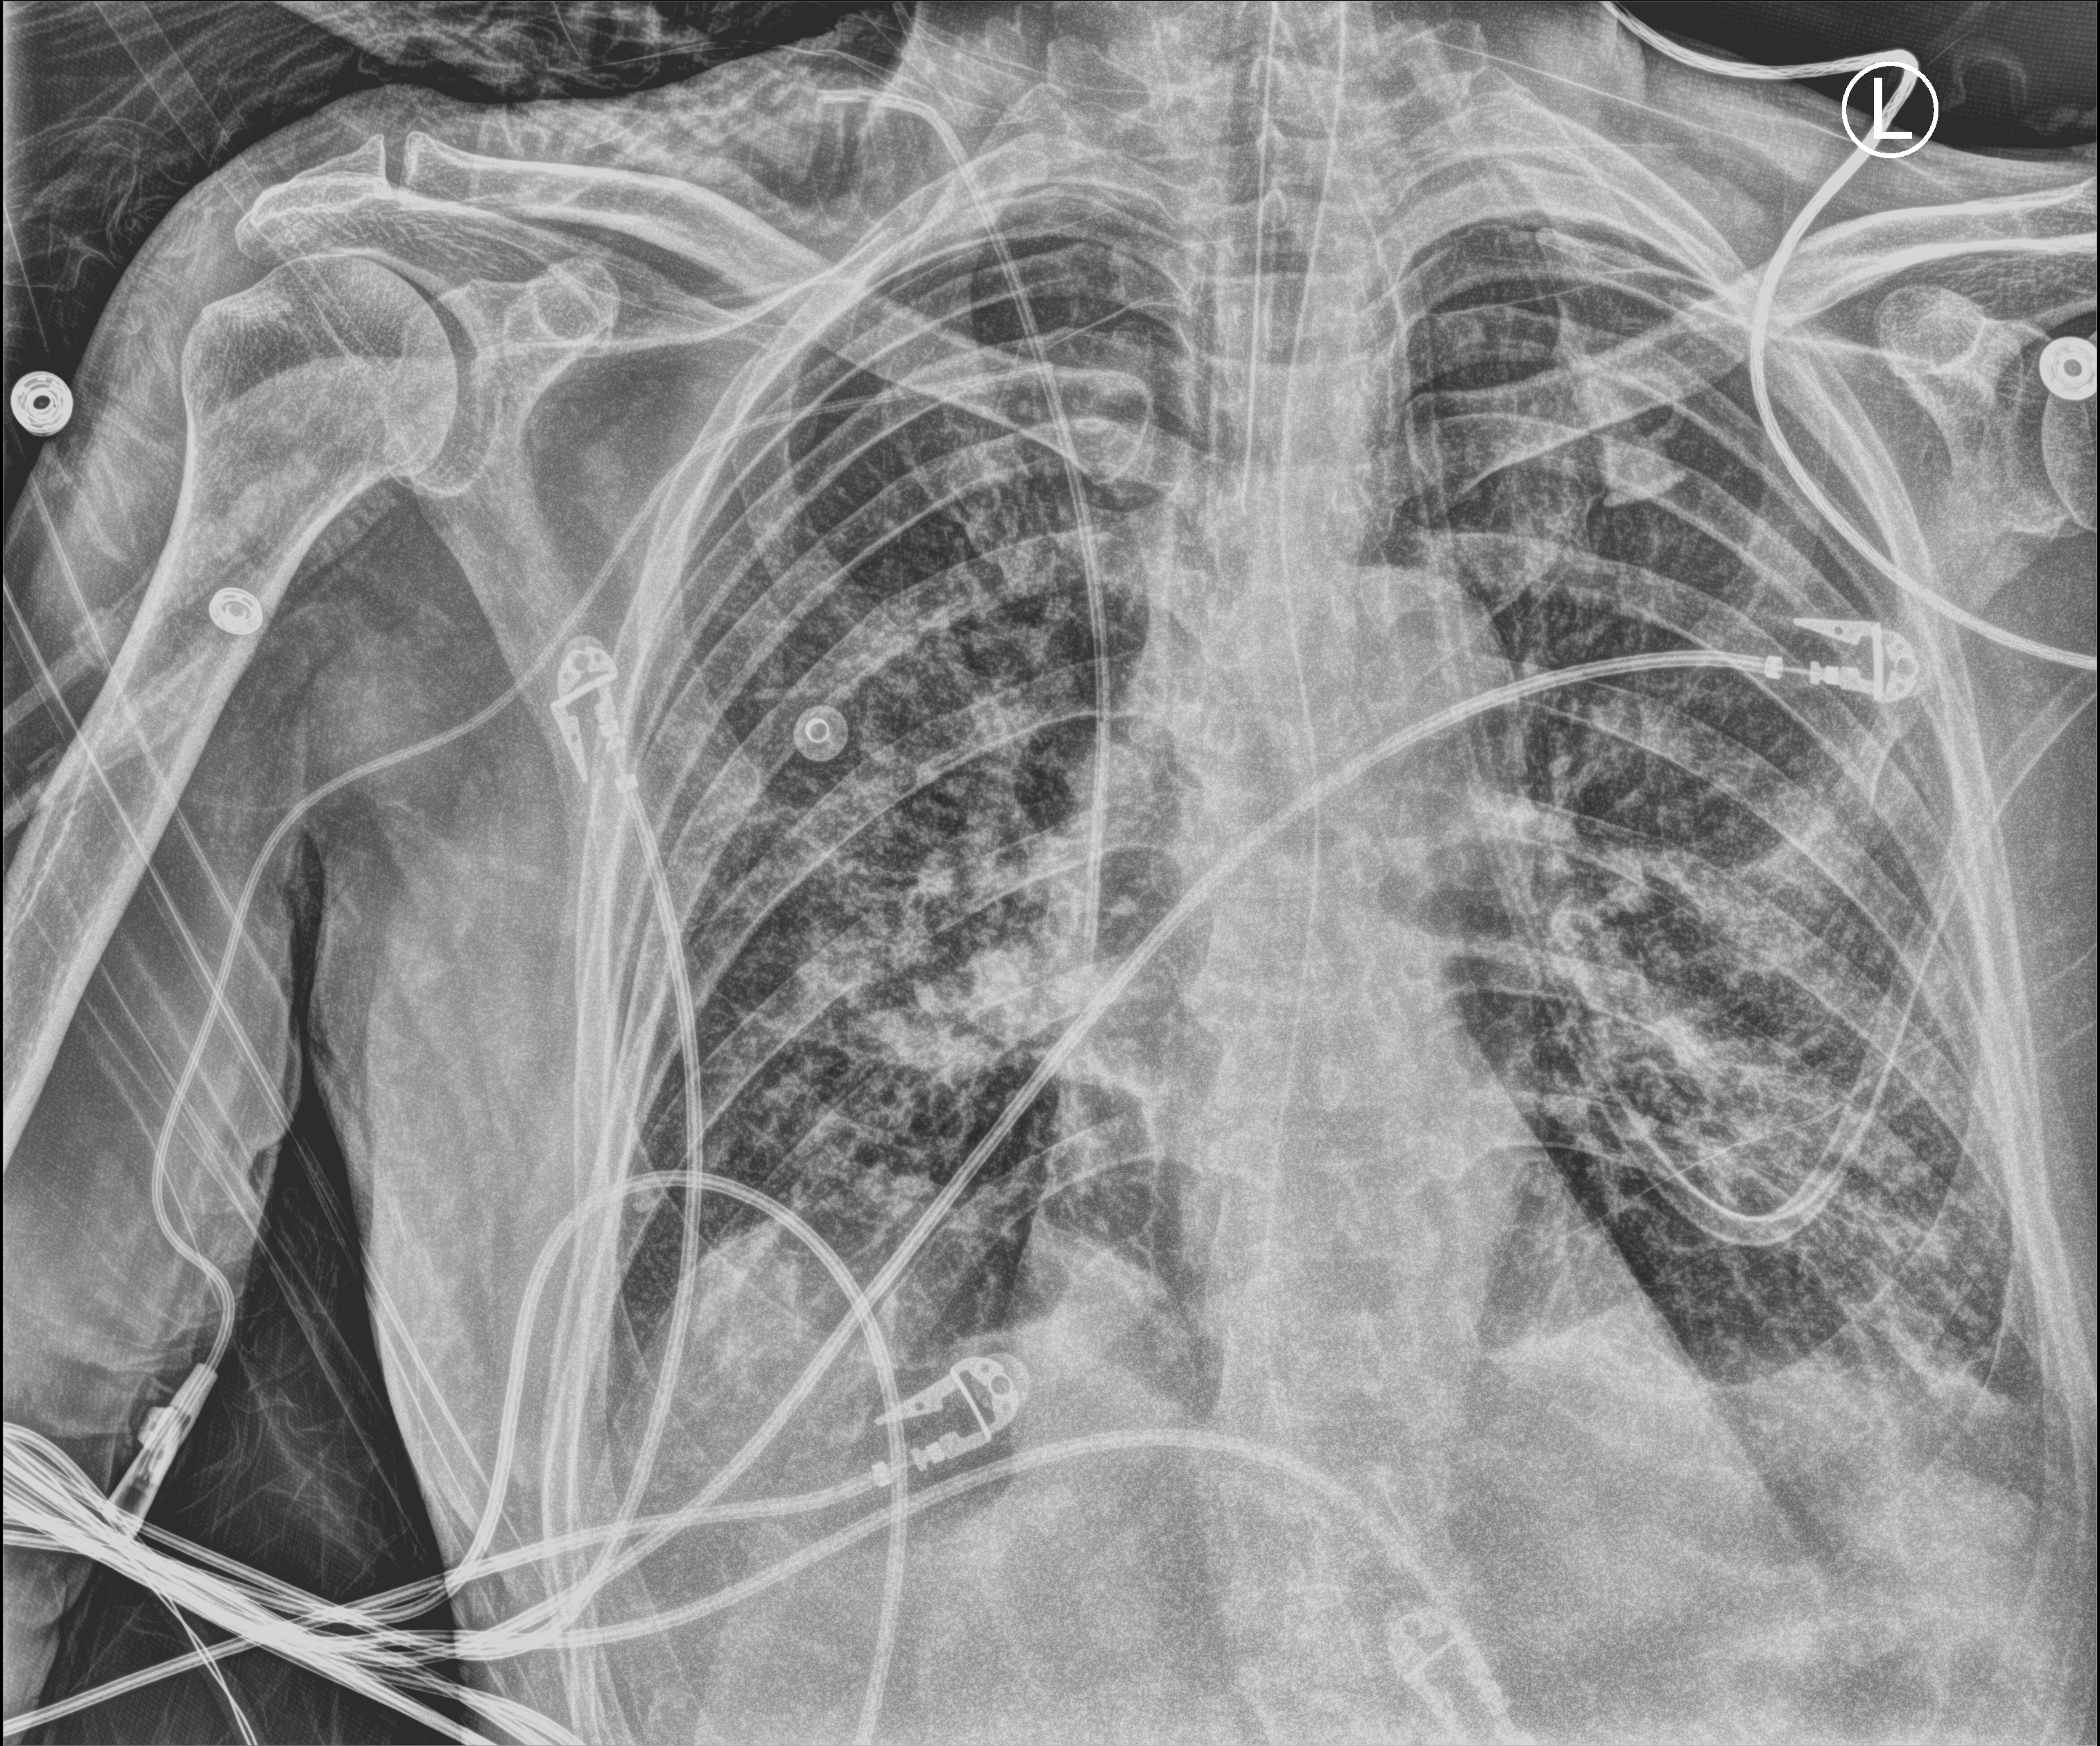
Bedside chest radiograph (computed radiography), anteroposterior (AP) projection. Male patient hospitalised with COVID-19, age 75–90 years.
From the hospital-stay record, not from the radiograph (when in the stay this image was taken is not recorded): COPD (admission record): no.